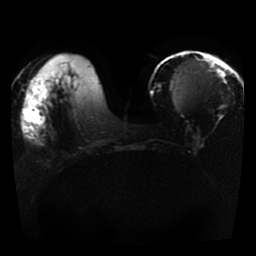
Breast MRI, one axial slice. Diffusion-weighted series; image 2 of 4 stored at this slice position (different b-values; order by instance number). 1.5 T. 256 × 256 image matrix, field of view 330 × 330 mm. Female patient.
Structures marked on this image (outlined manually by an expert reader):
- tumour on diffusion-weighted imaging: bounding box <34,90,57,103> (left, top, right, bottom; pixels)